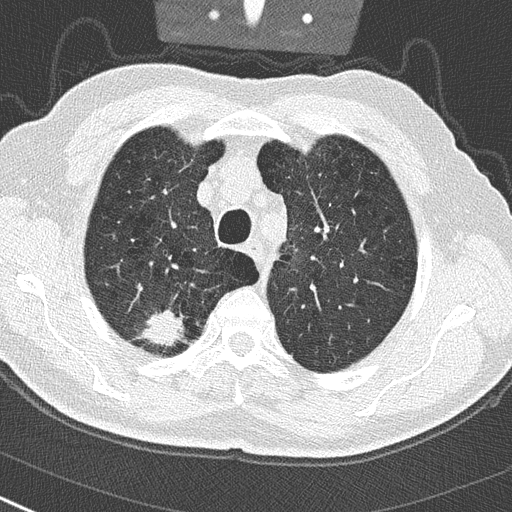
Low-dose screening chest CT, one axial slice; slice 233 of 290 in the series (ordered by position); reconstruction kernel B50f; 120 kVp; lung window (W 1500 / L -600 HU); 2 mm slice thickness; 512 × 512 image matrix, field of view 300 × 300 mm.
Annotated regions visible in this slice (manually delineated by an expert):
- lesion 1 (tumor, upper lobe of right lung): bounding box (x1, y1, x2, y2) in pixels: (142, 309, 185, 348)